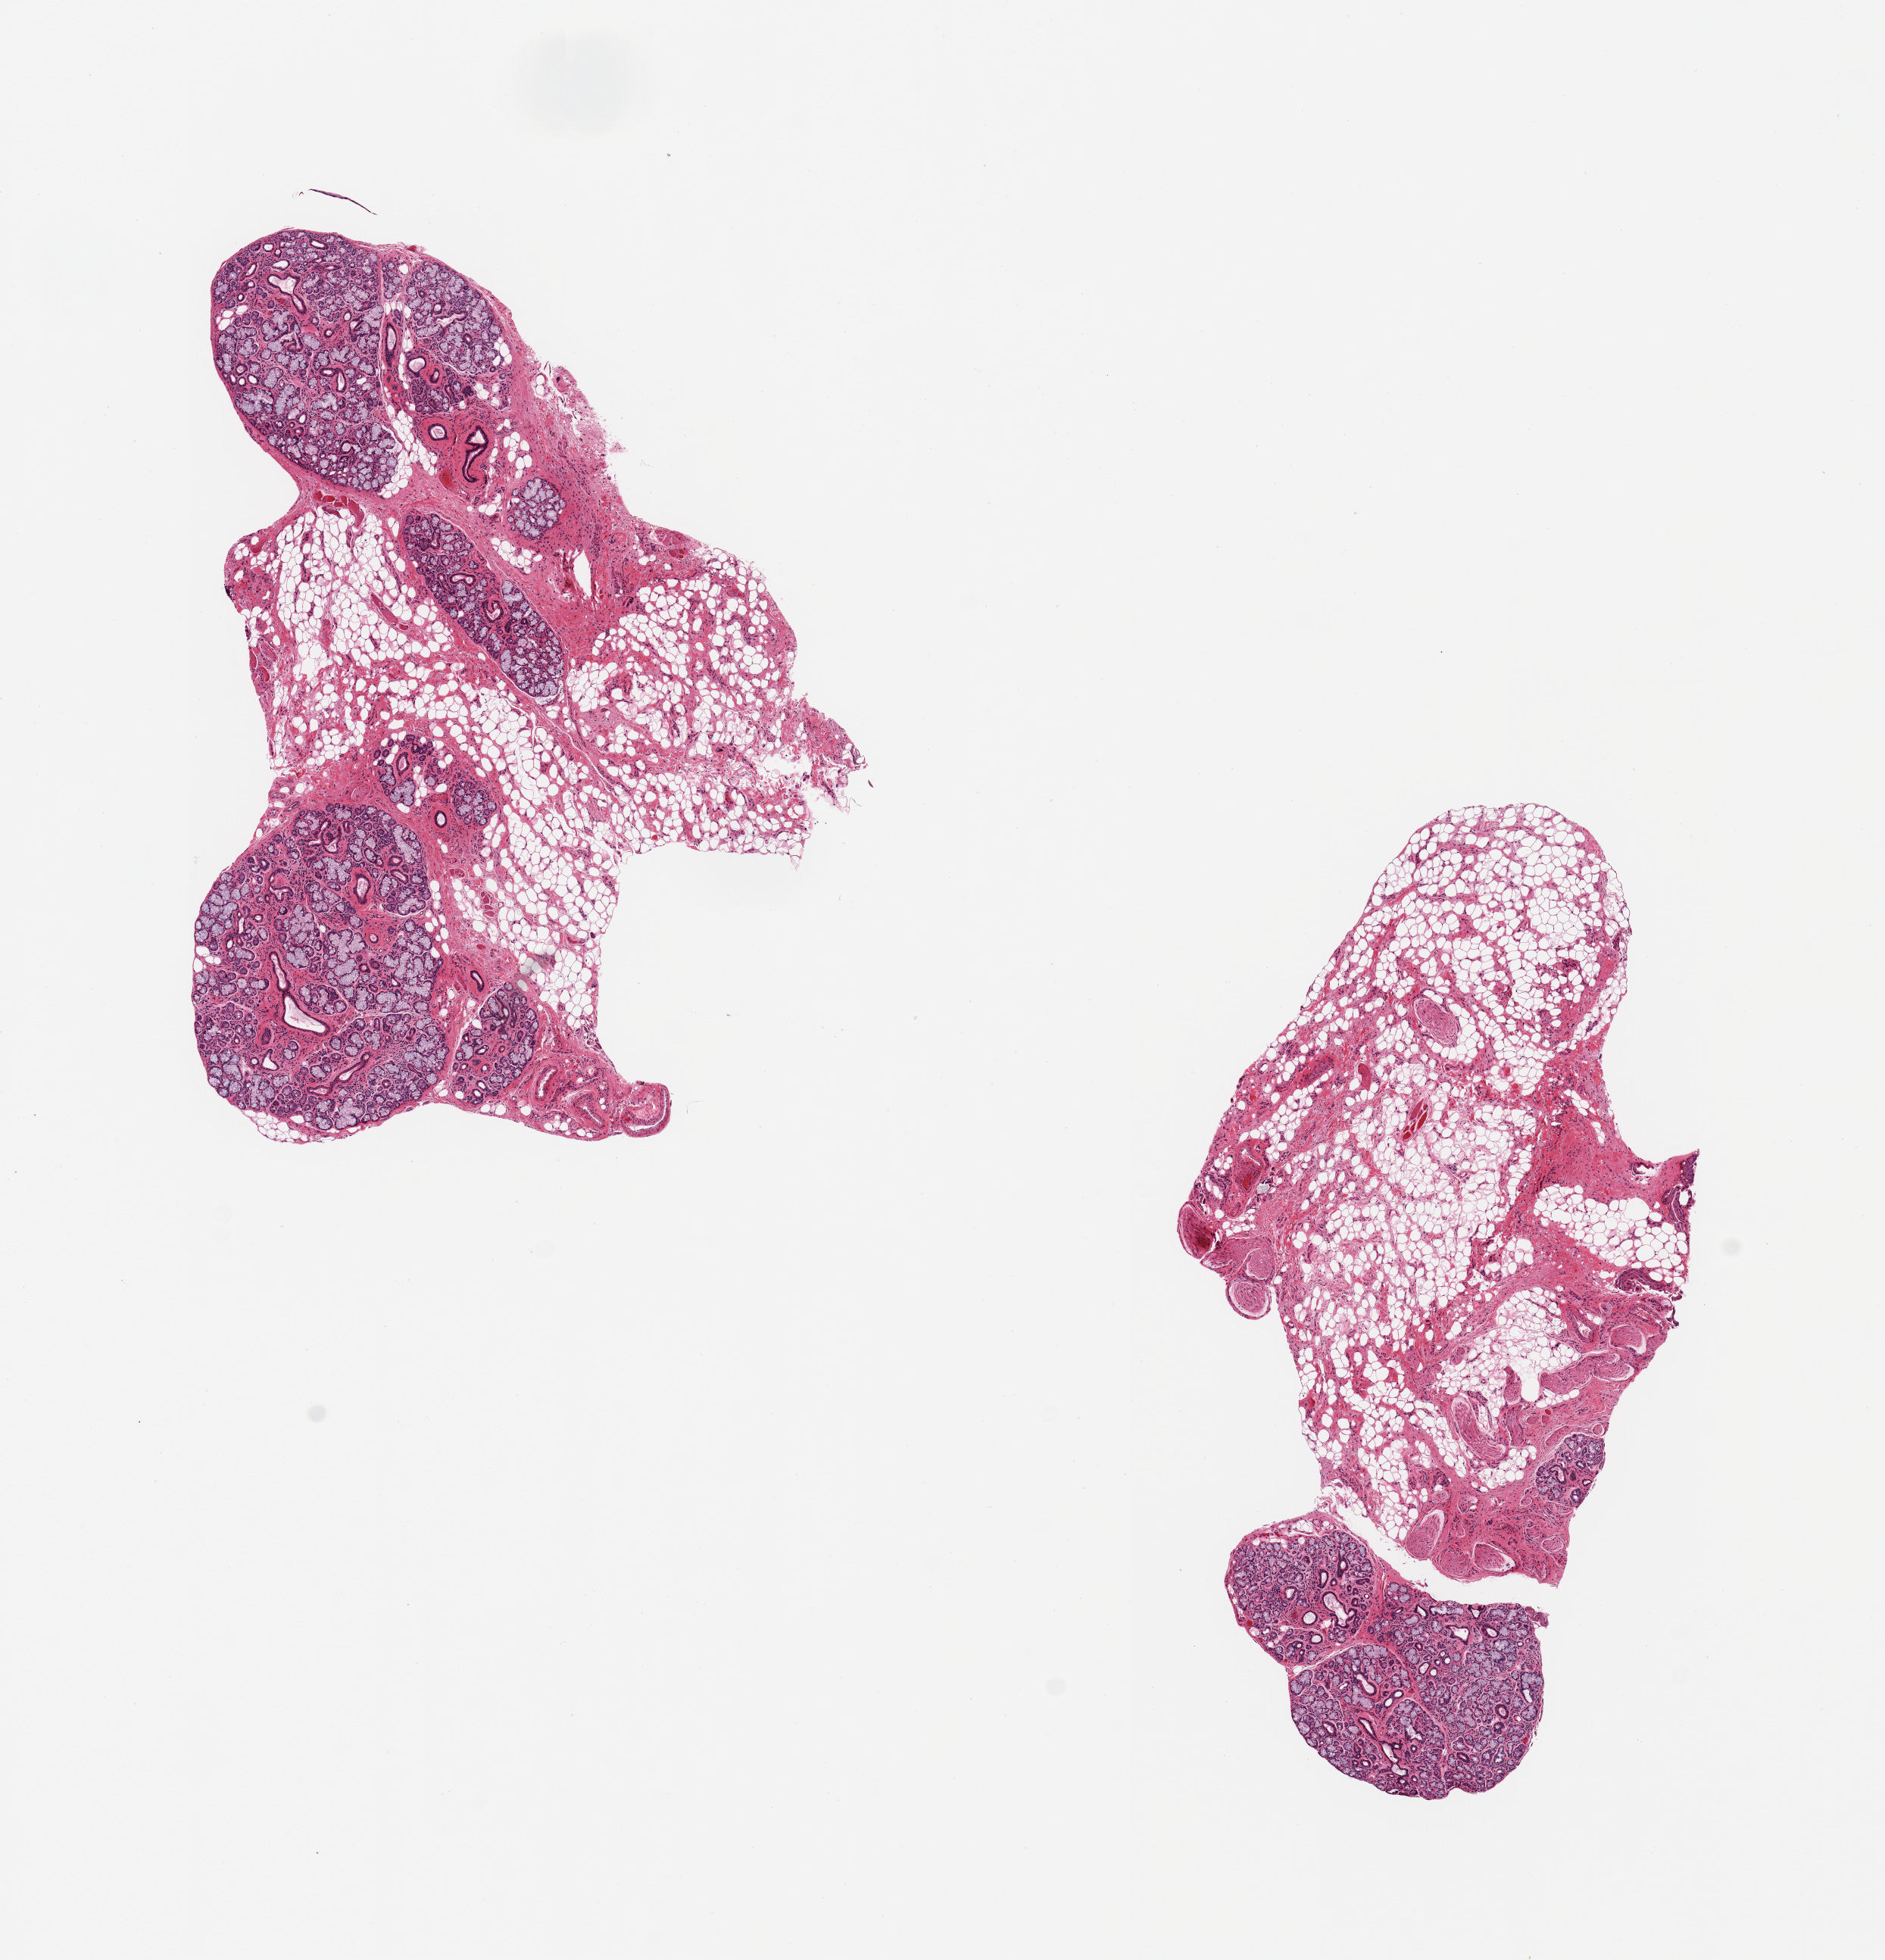
Digitized hematoxylin and eosin (H&E)-stained section, a low-resolution overview of the entire scanned area, about 9.8 x 10.2 mm (slide scanned at 20x). PAXgene-fixed paraffin-embedded (PFPE) section. Target tissue: minor salivary gland. Tissue donor sample. Donor: female.
Pathologist's review note for this sample: 2 pieces; 20 and 60% salivary gland elements, rest is mostly fat/nerve.